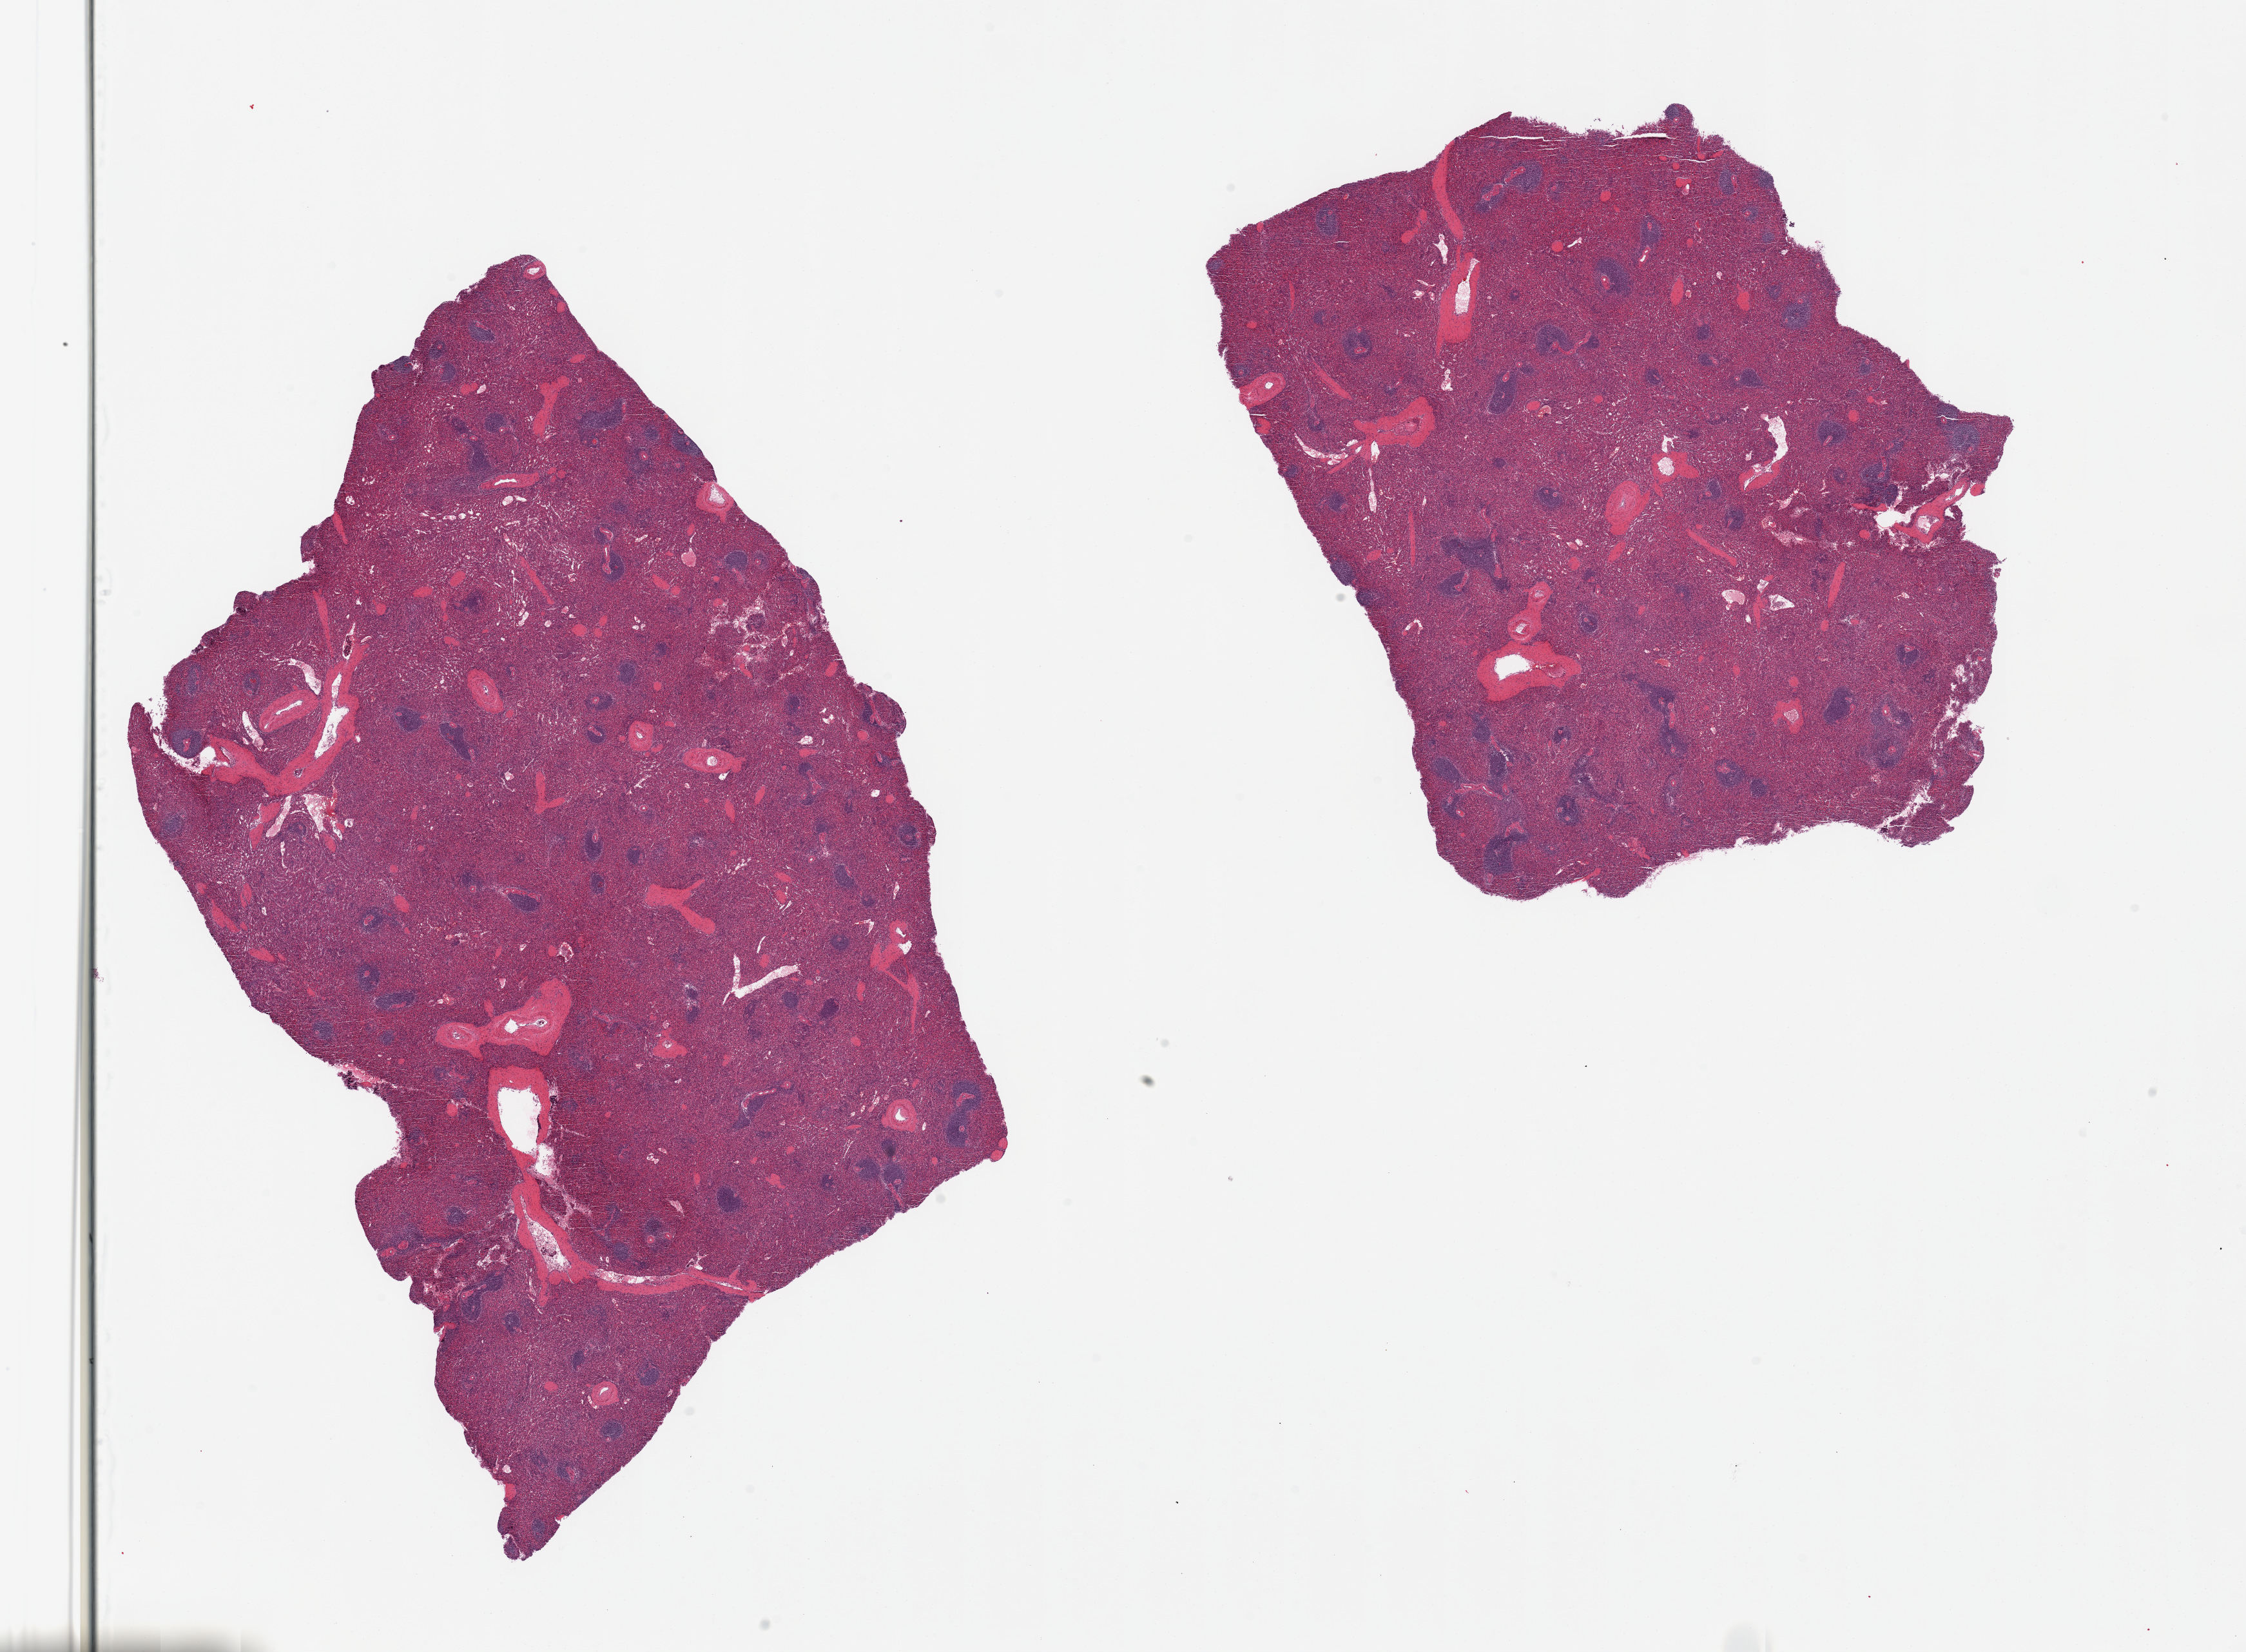
Whole-slide image, hematoxylin and eosin (H&E) stain — a low-resolution overview of the entire scanned area, about 27.6 x 20.3 mm (acquisition: 20x scan); PAXgene-fixed paraffin-embedded (PFPE) section; sampled site (target tissue): spleen; tissue donor sample. Donor sex: male.
Pathologist's review note for this sample: 2 pieces.